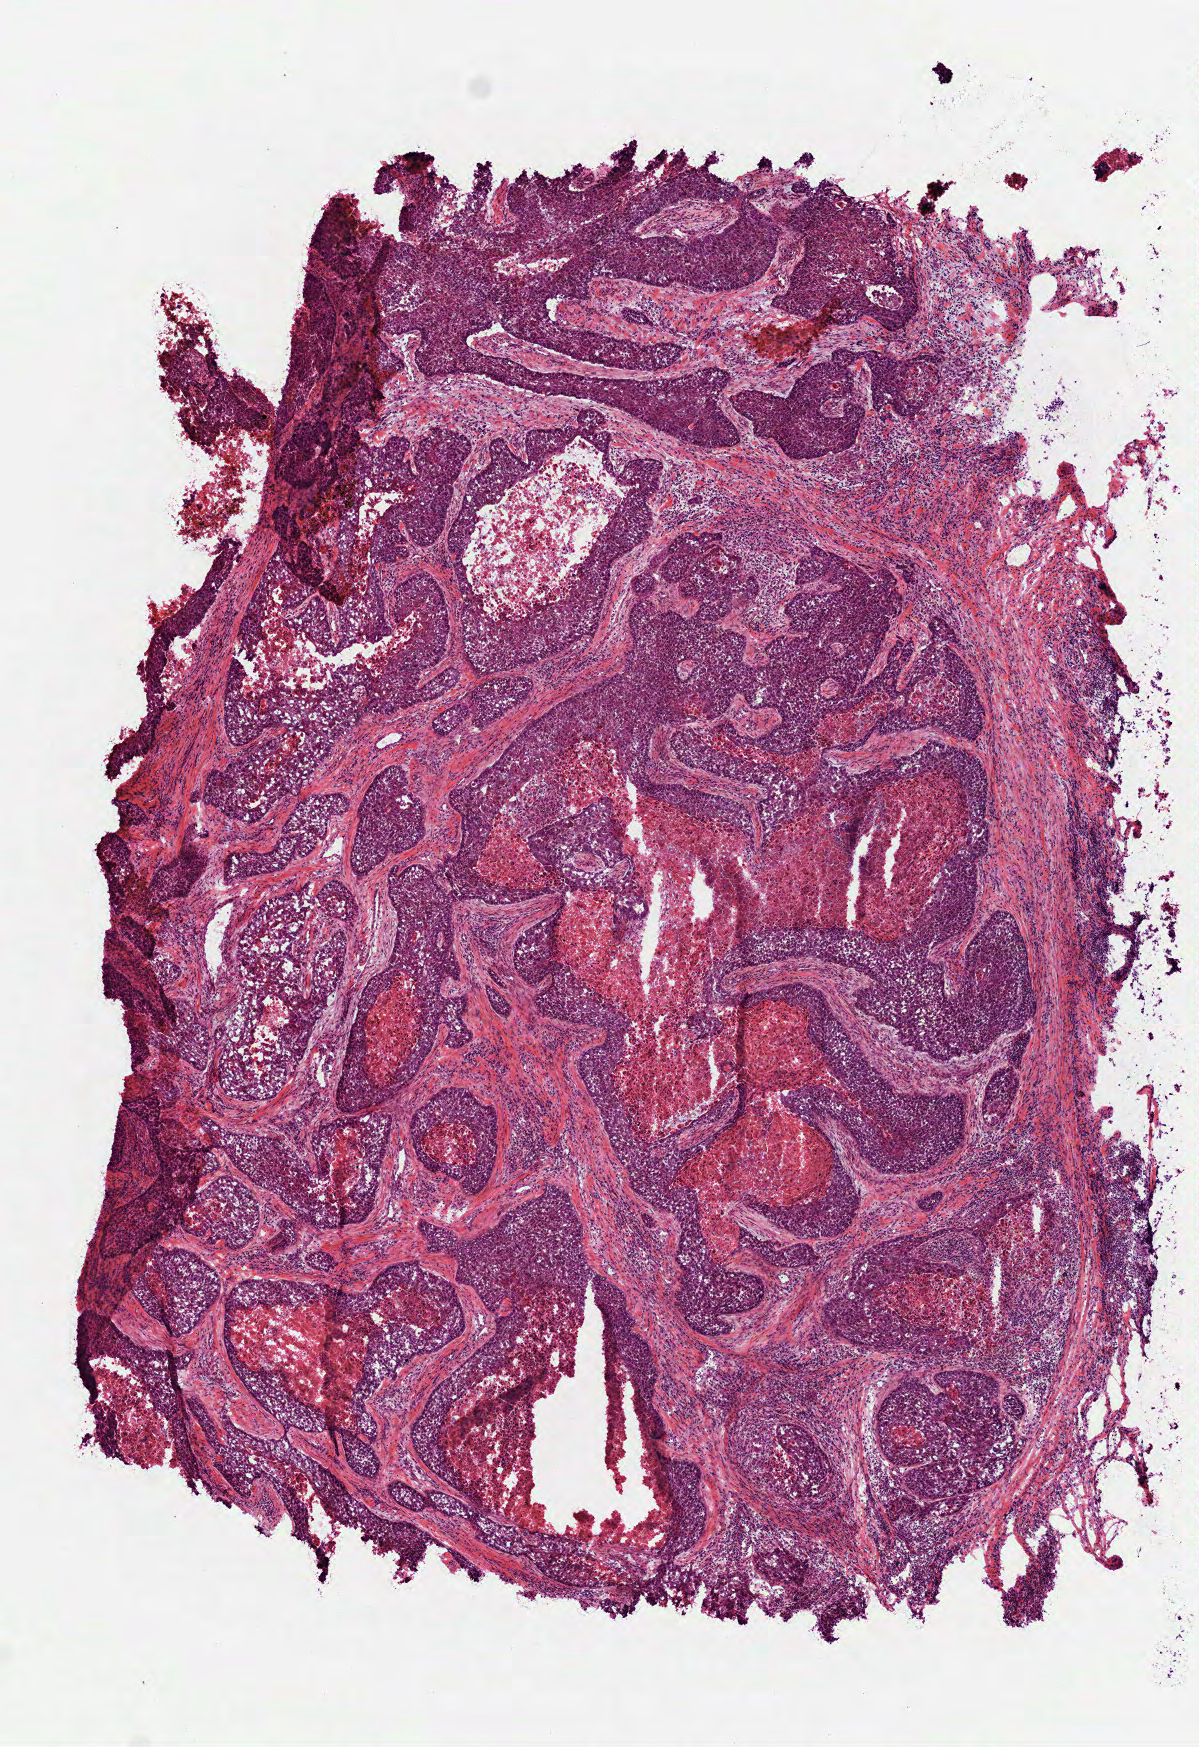
Whole-slide histology image, H&E-stained — shown as a low-resolution overview of the whole scanned area (about 4.8 x 7.0 mm, from a 40x scan), frozen section from the top of the tissue portion, lung, primary tumour sample. Patient: male, age at initial diagnosis 56 years.
Histologic diagnosis: Squamous cell carcinoma, NOS (lower lobe, lung).